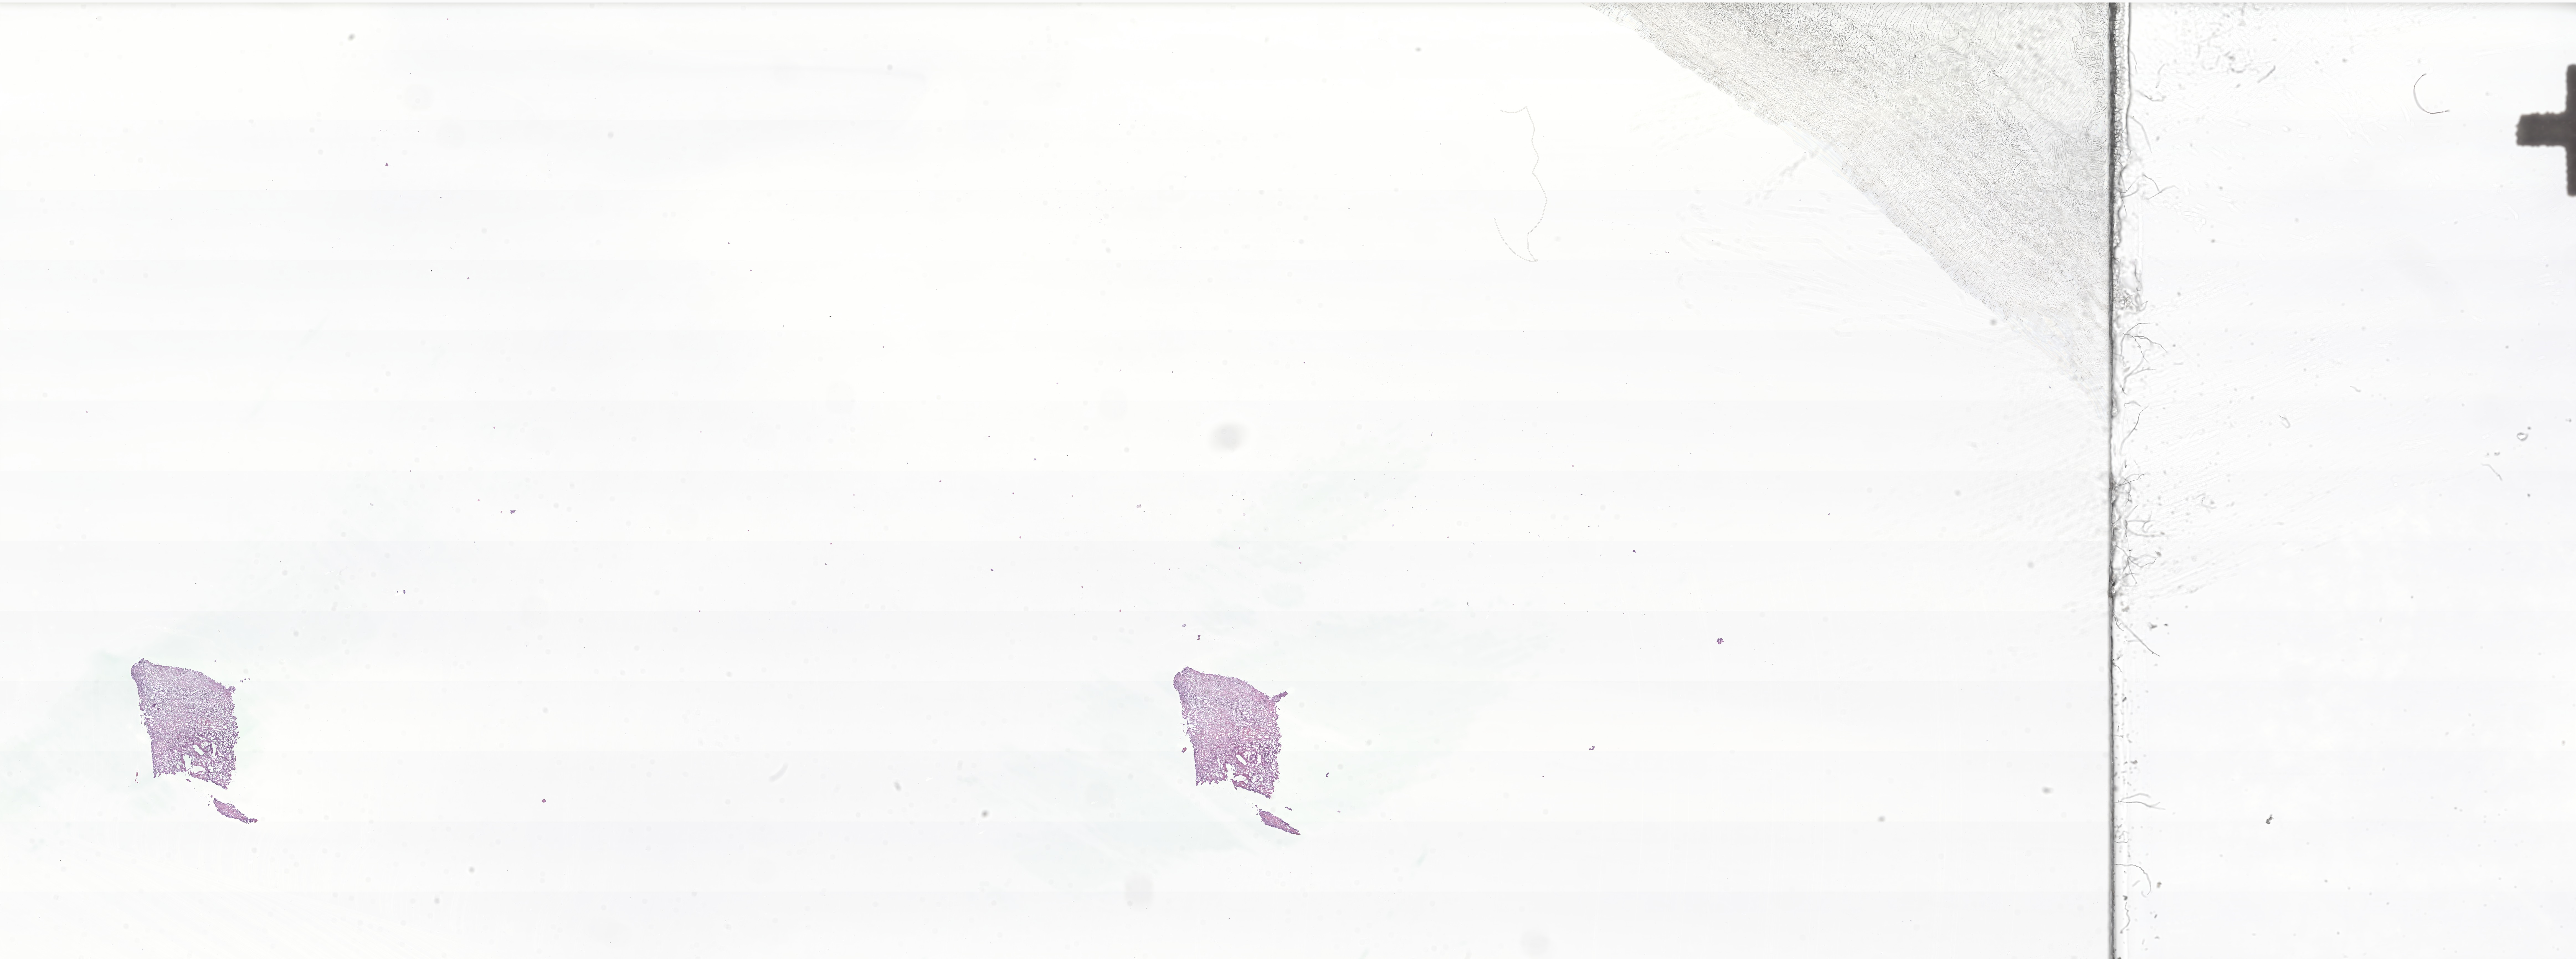
Whole-slide image, hematoxylin and eosin (H&E) stain of tumor tissue from the urinary system, whole scanned area (about 39.2 x 14.6 mm) shown as a low-resolution overview. Frozen section (OCT-embedded). Male patient, age 177 months (14 years 9 months).
Diagnosis: Rhabdomyosarcoma, NOS.